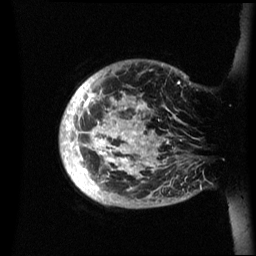
Breast MRI (dynamic contrast-enhanced), one sagittal slice. Position 7 of 60 along the scan axis. Dynamic contrast-enhanced series, image 2 of 3 at this slice position (ordered by acquisition). 1.5 T. TE 4.2 ms, TR 8.4 ms. 2.4 mm slice thickness. 256 × 256 image matrix, field of view 230 × 230 mm. Patient: female, 48 years.
Outlined on this slice (semi-automatically segmented with operator editing):
- analysis volume of interest (the breast-tissue region the enhancement analysis was run in; not a lesion): bounding box <59,60,201,208> (left, top, right, bottom; pixels)
- tumour enhancement mask (voxels above the 70 % enhancement threshold inside the analysis volume of interest): <60,81,180,191>